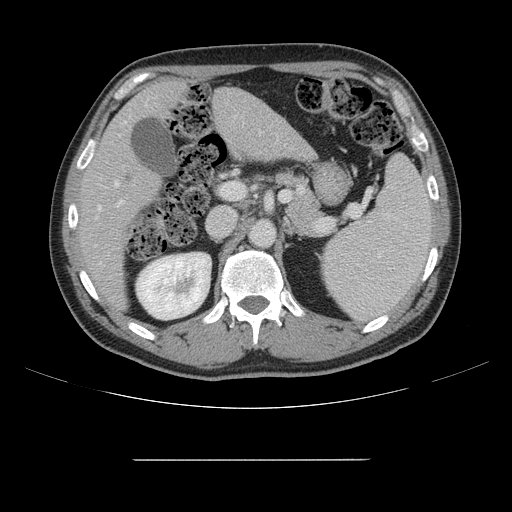
Contrast-enhanced abdominal CT, one axial slice. Slice 86 of 164 in the series (ordered by position). 120 kVp. Intravenous contrast given. Soft-tissue window (W 400 / L 40 HU). 512 × 512 image matrix. Male patient, age 54 years. Case-level facts recorded for this patient, not image findings: diagnosis: colorectal cancer liver metastases, imaged before liver resection.
Annotated regions visible in this slice (outlined manually by an expert reader):
- hepatic veins: bounding box [x1, y1, x2, y2] px = [98, 181, 119, 264]
- liver: [81, 81, 309, 304]
- planned liver remnant (the part of the liver to remain after resection): [81, 82, 229, 305]
- portal vein (with intrahepatic branches): [117, 122, 126, 206]